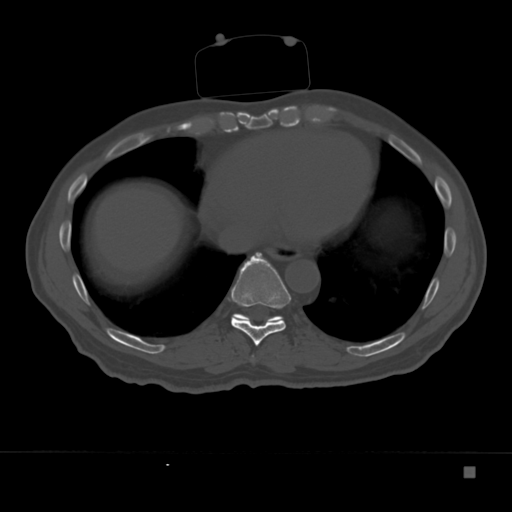
CT including the spine, one axial slice. Slice 186 of 332 in the series (ordered by position). Reconstruction kernel Br40s. Bone window (W 1800 / L 400 HU). 1.5 mm slice thickness. 512 × 512 image matrix. Patient: male, 72 years. From the clinical record (not read from this slice): primary cancer: skeletal.
Structures marked on this image (semi-automatic segmentation, software-assisted and operator-edited):
- T9 vertebra: box from (x=231, y=252) to (x=291, y=346) px